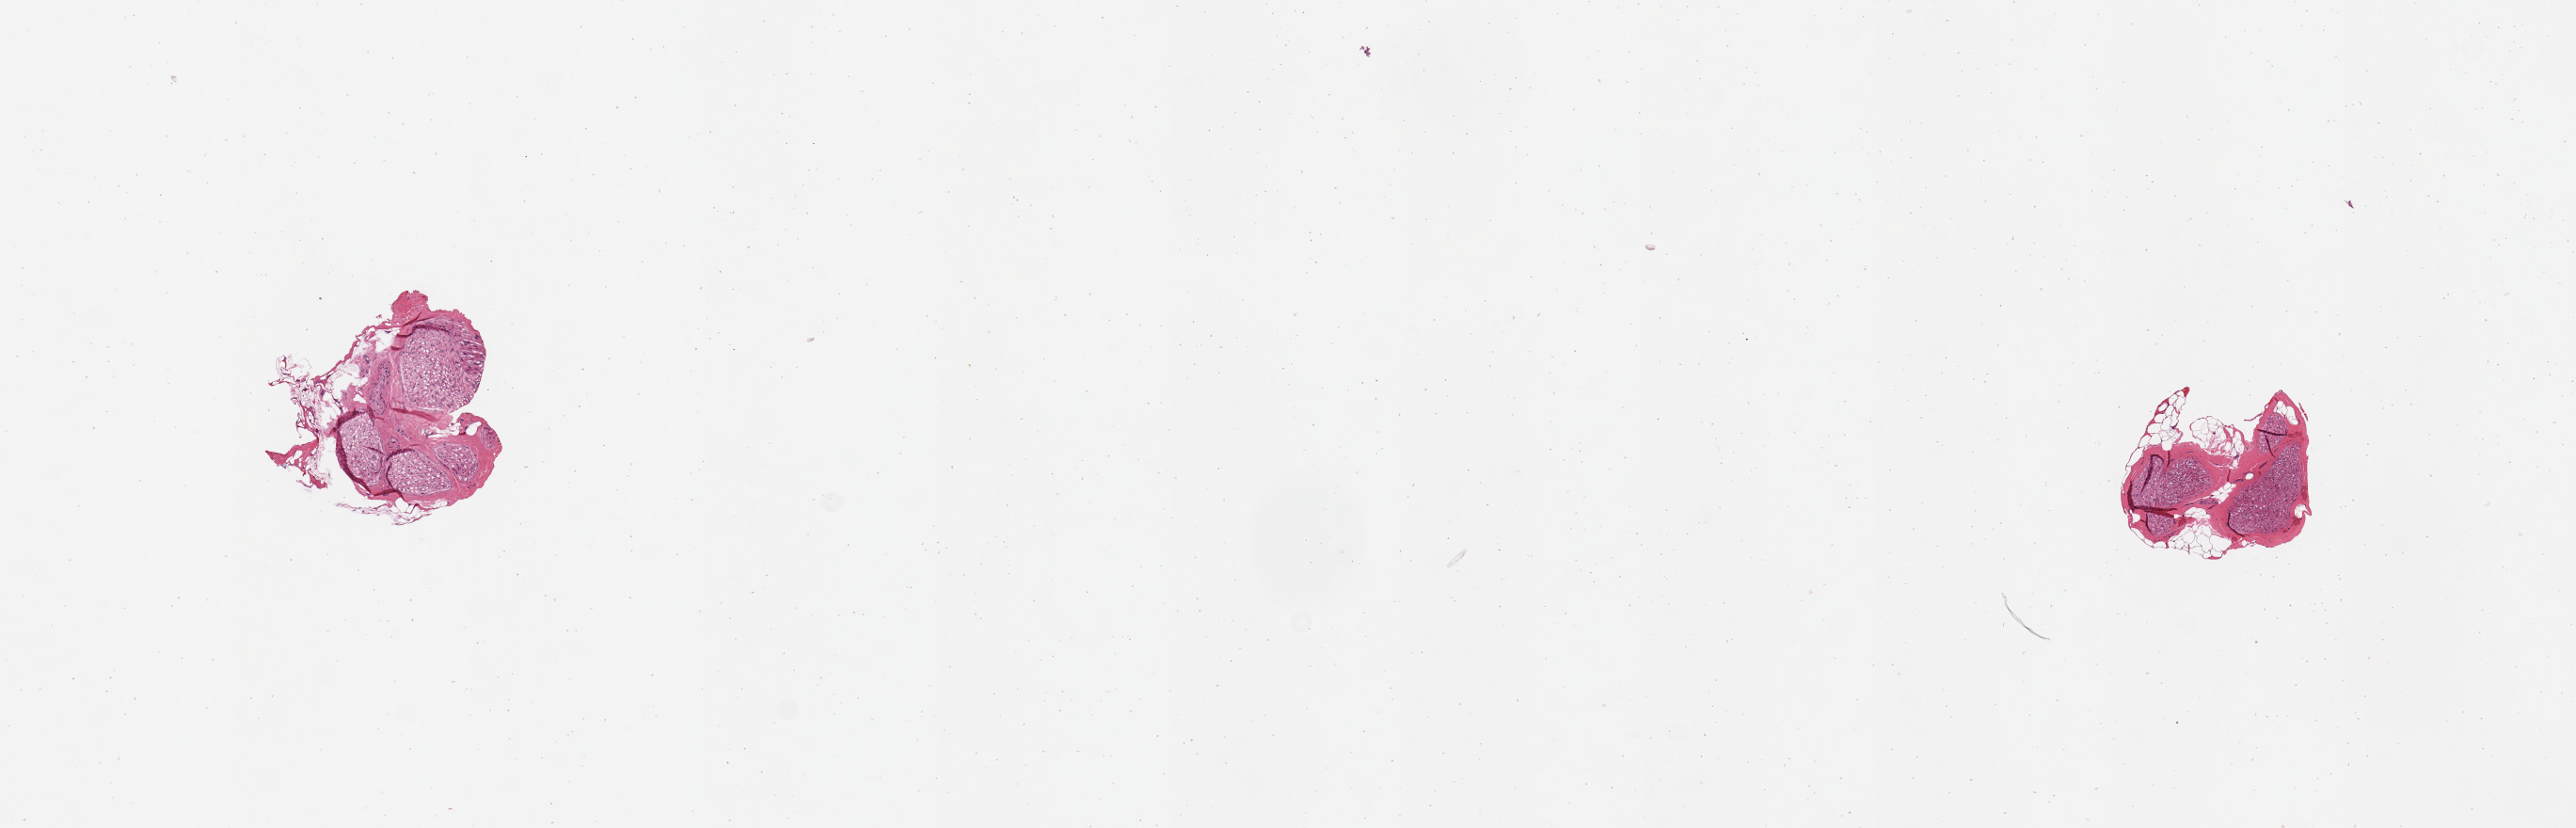
Digitized H&E-stained section — low-resolution overview of the scanned area, about 10.8 x 3.5 mm (from a 20x scan); PAXgene-fixed paraffin-embedded (PFPE) section; target tissue: tibial nerve; tissue donor sample.
Pathologist's review note for this sample: 2 pieces; adherent fat/fibrous tissue up to ~0.2mm.